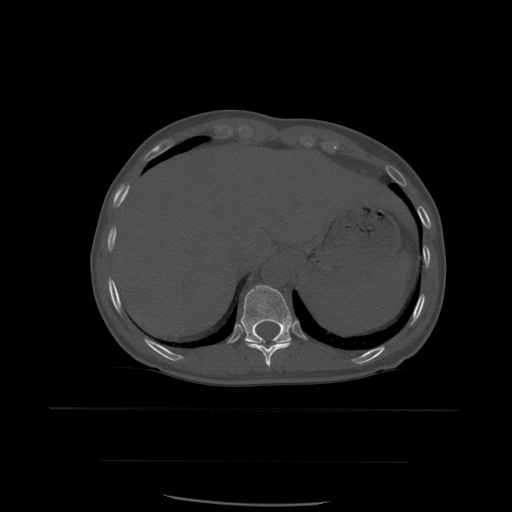
CT including the spine, one axial slice; position 304 of 574 along the scan axis; bone window (W 1800 / L 400 HU); 1.25 mm slice thickness; 512 × 512 image matrix, field of view 392 × 392 mm. Patient age 48 years. From the clinical record (not read from this slice): primary cancer: lung.
Structures marked on this image (semi-automatic segmentation, software-assisted and operator-edited):
- T10 vertebra: bounding box (x1, y1, x2, y2) in pixels: (246, 342, 291, 368)
- T11 vertebra: (241, 285, 294, 345)